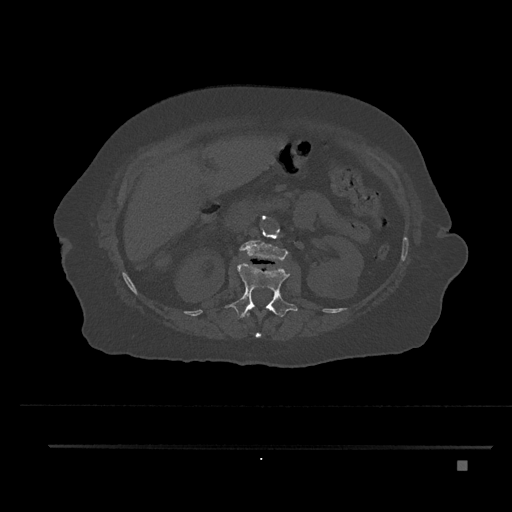
CT including the spine, one axial slice. Slice 218 of 797 in the series (ordered by position). Reconstruction kernel Br40s/3. 120 kVp. Bone window (W 1800 / L 400 HU). 0.5 mm slice thickness. 512 × 512 image matrix, field of view 437 × 437 mm. Patient: female, 76 years. Case-level facts recorded for this patient, not image findings: primary cancer: lung; vertebrae with lytic lesions (as recorded): T11, L3.
Annotated regions visible in this slice (semi-automatic segmentation, software-assisted and operator-edited):
- L1 vertebra: box from (x=226, y=262) to (x=298, y=320) px
- L2 vertebra: (x=240, y=240)–(x=288, y=260)
- T12 vertebra: (x=245, y=311)–(x=275, y=338)